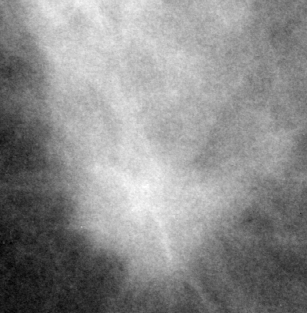
Region of interest cut from a scanned film mammogram (one marked finding), right breast, CC view, BI-RADS breast density category 3 (scale 1–4).
- Marked abnormality: mass, shape irregular / architectural distortion, margins spiculated; BI-RADS assessment category 5; pathology result (as recorded, not read from the image): malignant.